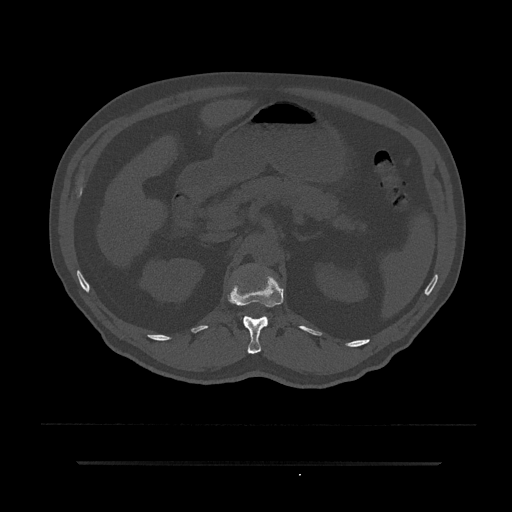
CT including the spine, one axial slice; position 188 of 797 along the scan axis; 120 kVp; bone window (W 1800 / L 400 HU); 0.5 mm slice thickness; 512 × 512 image matrix. Male patient, age 59 years. From the clinical record (not read from this slice): primary cancer: bile ducts.
Outlined on this slice (semi-automatic segmentation, software-assisted and operator-edited):
- L1 vertebra: bounding box <243,316,268,318> (left, top, right, bottom; pixels)
- T12 vertebra: <228,272,284,354>